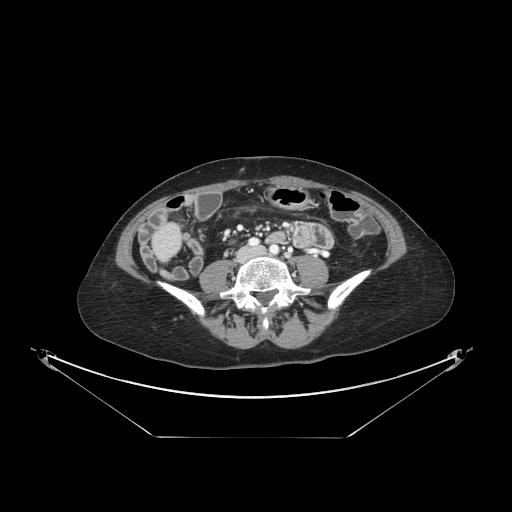
Contrast-enhanced abdominal CT, one axial slice. Slice 19 of 148 in the series (ordered by position). Reconstruction kernel STANDARD. Intravenous contrast given. Soft-tissue window (W 400 / L 40 HU). 2.5 mm slice thickness. 512 × 512 image matrix. Female patient, age 73 years. From the clinical record (not read from this slice): diagnosis: colorectal cancer liver metastases, imaged before liver resection; multiple liver metastases: no; largest metastasis: 1 cm.
Outlined on this slice (manually delineated by an expert):
- liver: bounding box (x1, y1, x2, y2) in pixels: (155, 227, 180, 258)